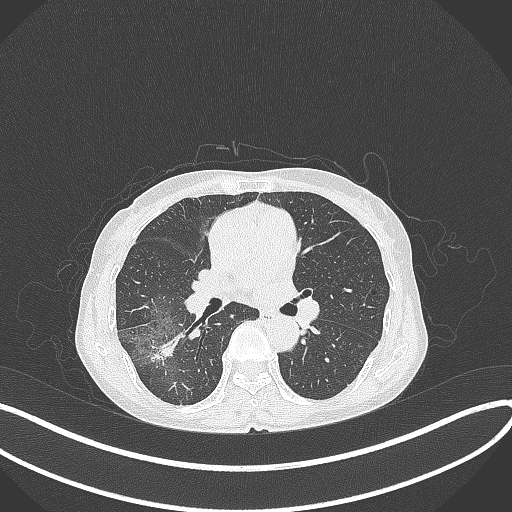
Chest CT, one axial slice; slice 216 of 371 in the series (ordered by position); 120 kVp; lung window (W 1500 / L -600 HU); 1 mm slice thickness; 512 × 512 image matrix, field of view 400 × 400 mm. Female patient, age 69 years. From the clinical record (not read from this slice): clinical TNM (as recorded): T1b N0 M0; histopathological grade: G2-3.
Annotated regions visible in this slice (bounding box drawn by a radiologist):
- lung tumour (recorded histology: adenocarcinoma): bounding box (x1, y1, x2, y2) in pixels: (148, 332, 179, 365)